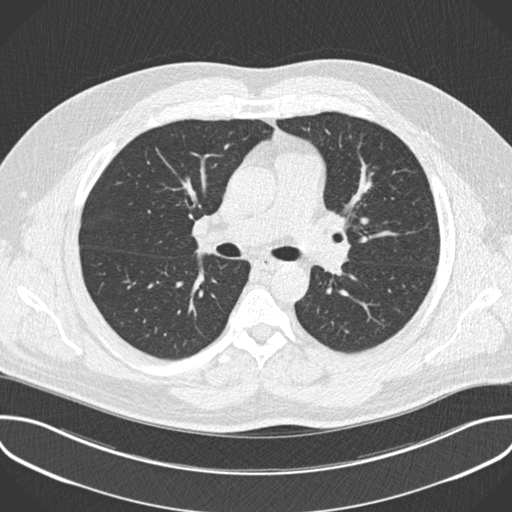
Chest CT (low-dose screening protocol), one axial image. First (baseline) screen. Lung window (W 1500 / L -600 HU). 2 mm slice thickness. Standard (soft-tissue) reconstruction kernel (B30f). 512 × 512 image matrix. Male, age 55 years at enrolment. Former smoker at enrolment.
- Lesion marked by an expert reader, bounding box <348,160,390,195> (left, top, right, bottom; pixels).
- Reader record for this screening exam (exam-level; its link to the box is not recorded): non-calcified nodule or mass ≥4 mm, lingula, 13 × 12 mm, spiculated (stellate) margins, soft tissue attenuation.
- Lung cancer was diagnosed 169 days after this screen: adenocarcinoma, NOS, left upper lobe, stage IA (AJCC 6th edition), 13 mm at pathology.